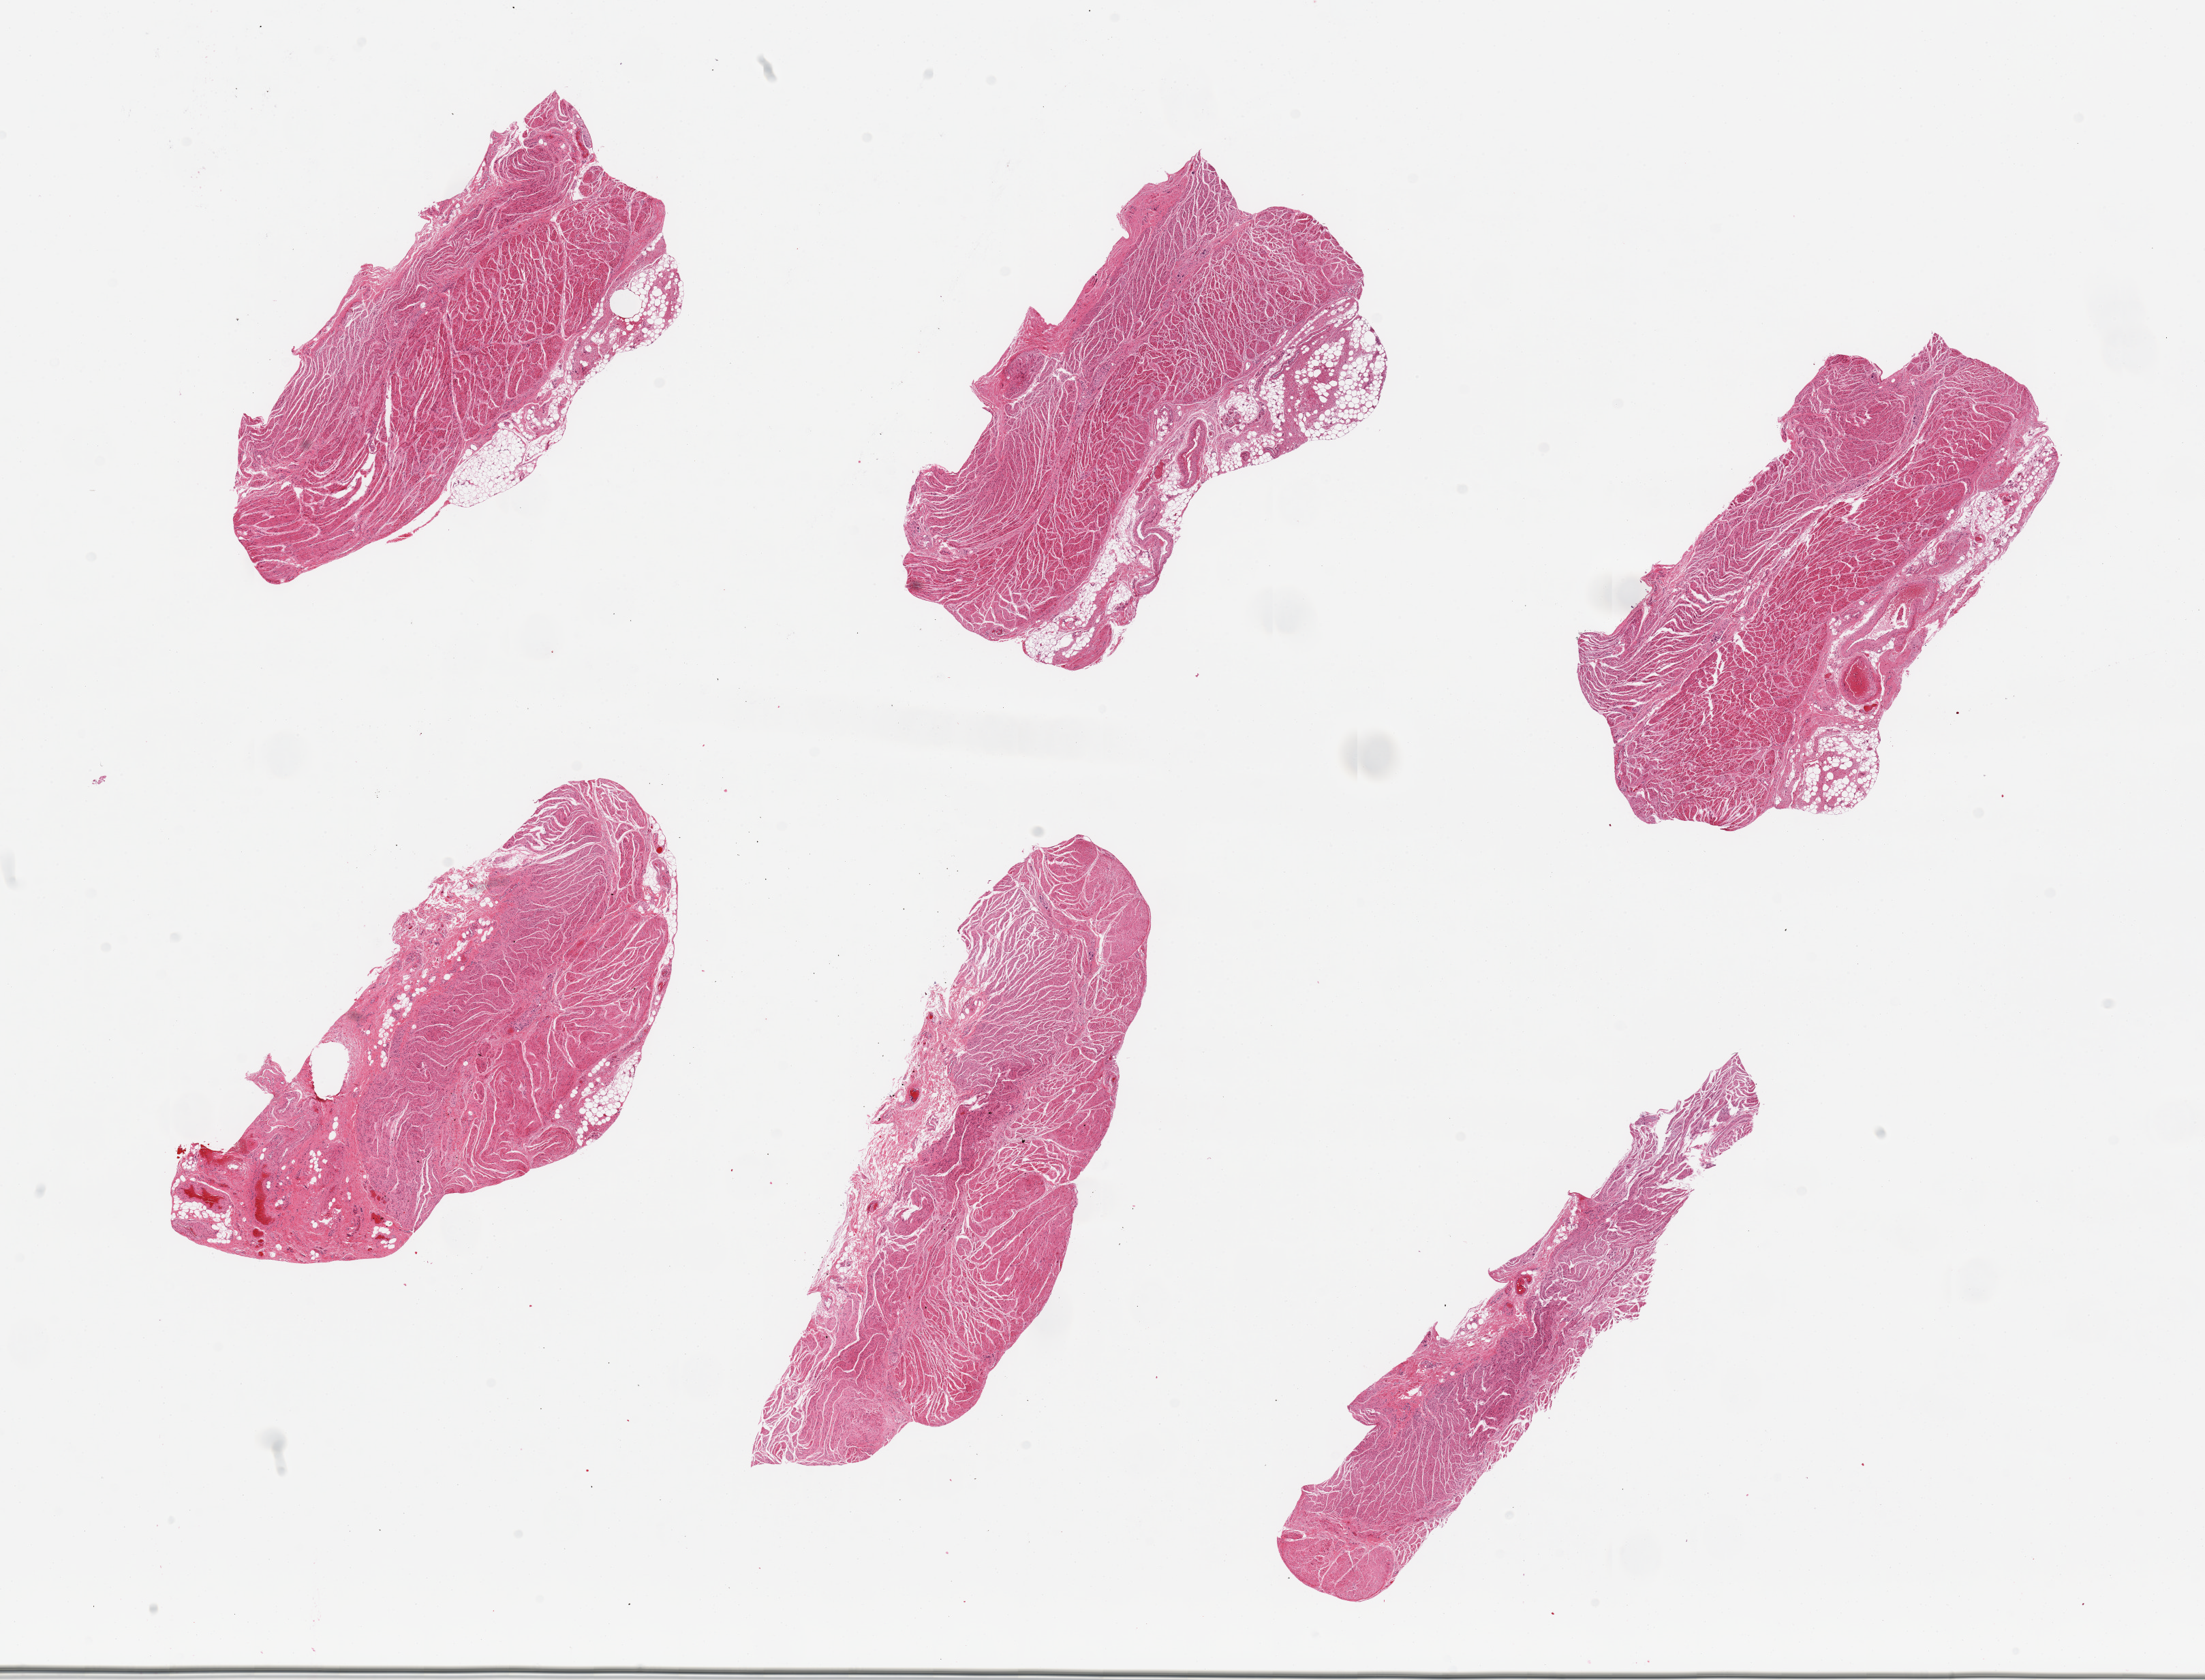
Whole-slide image, haematoxylin and eosin stain — shown as a low-resolution overview of the whole scanned area (about 25.6 x 19.5 mm), PAXgene-fixed paraffin-embedded (PFPE) section, section of gastroesophageal junction (target tissue), tissue donor sample.
Review note (as recorded): 6 pieces.